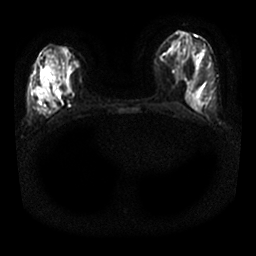
Breast MRI, one axial slice; position 8 of 25 along the scan axis; diffusion-weighted series; image 2 of 4 stored at this slice position (different b-values; order by instance number); 1.5 T; 256 × 256 image matrix, field of view 330 × 330 mm. Female patient.
Structures marked on this image (expert manual segmentation):
- tumour on diffusion-weighted imaging: bounding box [x1, y1, x2, y2] px = [56, 85, 70, 95]